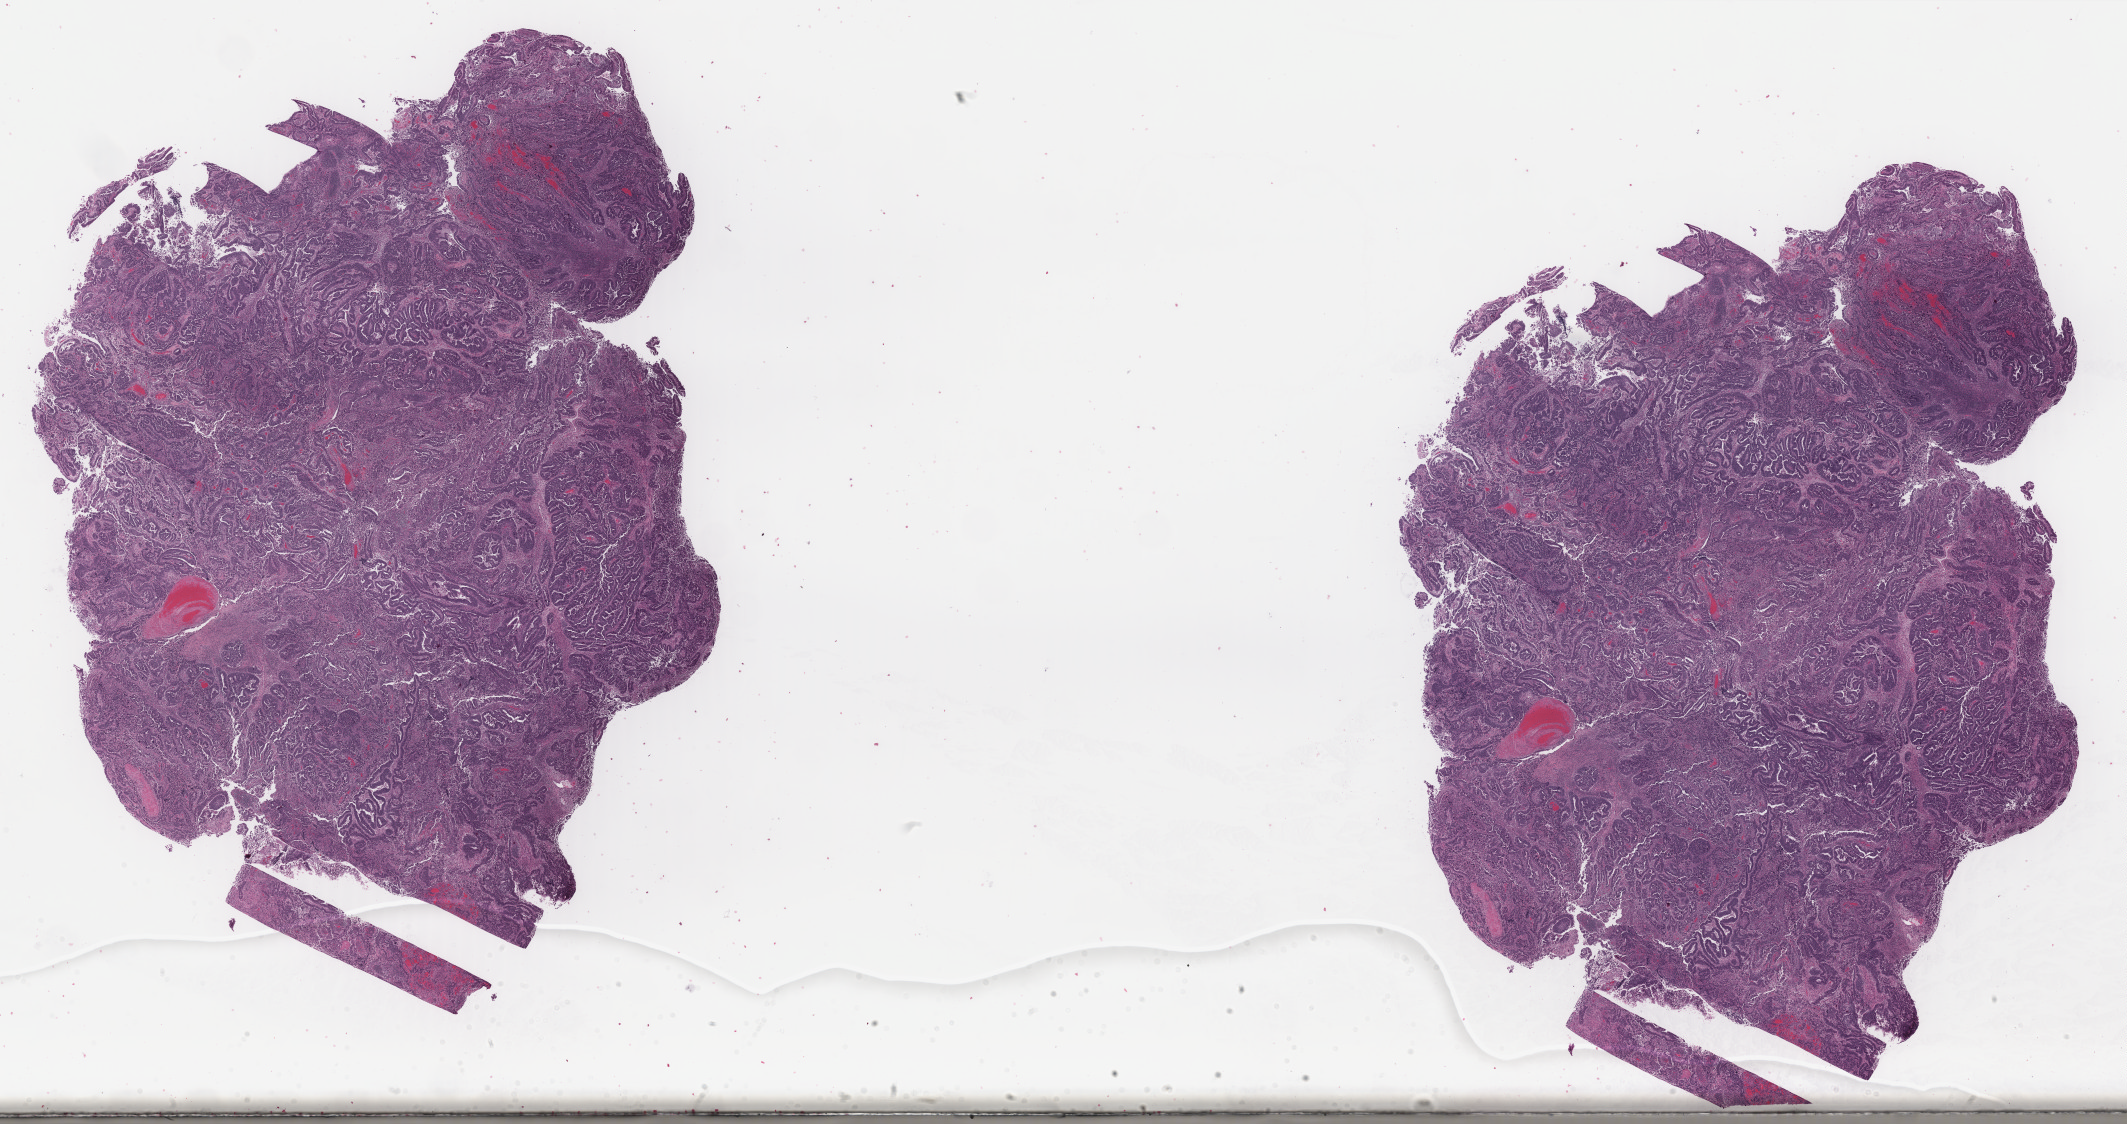
H&E-stained whole-slide image — low-resolution overview of the scanned area, about 33.7 x 17.8 mm, FFPE section, primary tumour sample from the uterus. Female patient; age at initial diagnosis 67 years. Histologic grade: G3 (poorly differentiated).
Histologic diagnosis: Endometrioid adenocarcinoma, NOS. FIGO stage: IIIC2. Lymph nodes positive (case pathology): 4 of 16 examined.